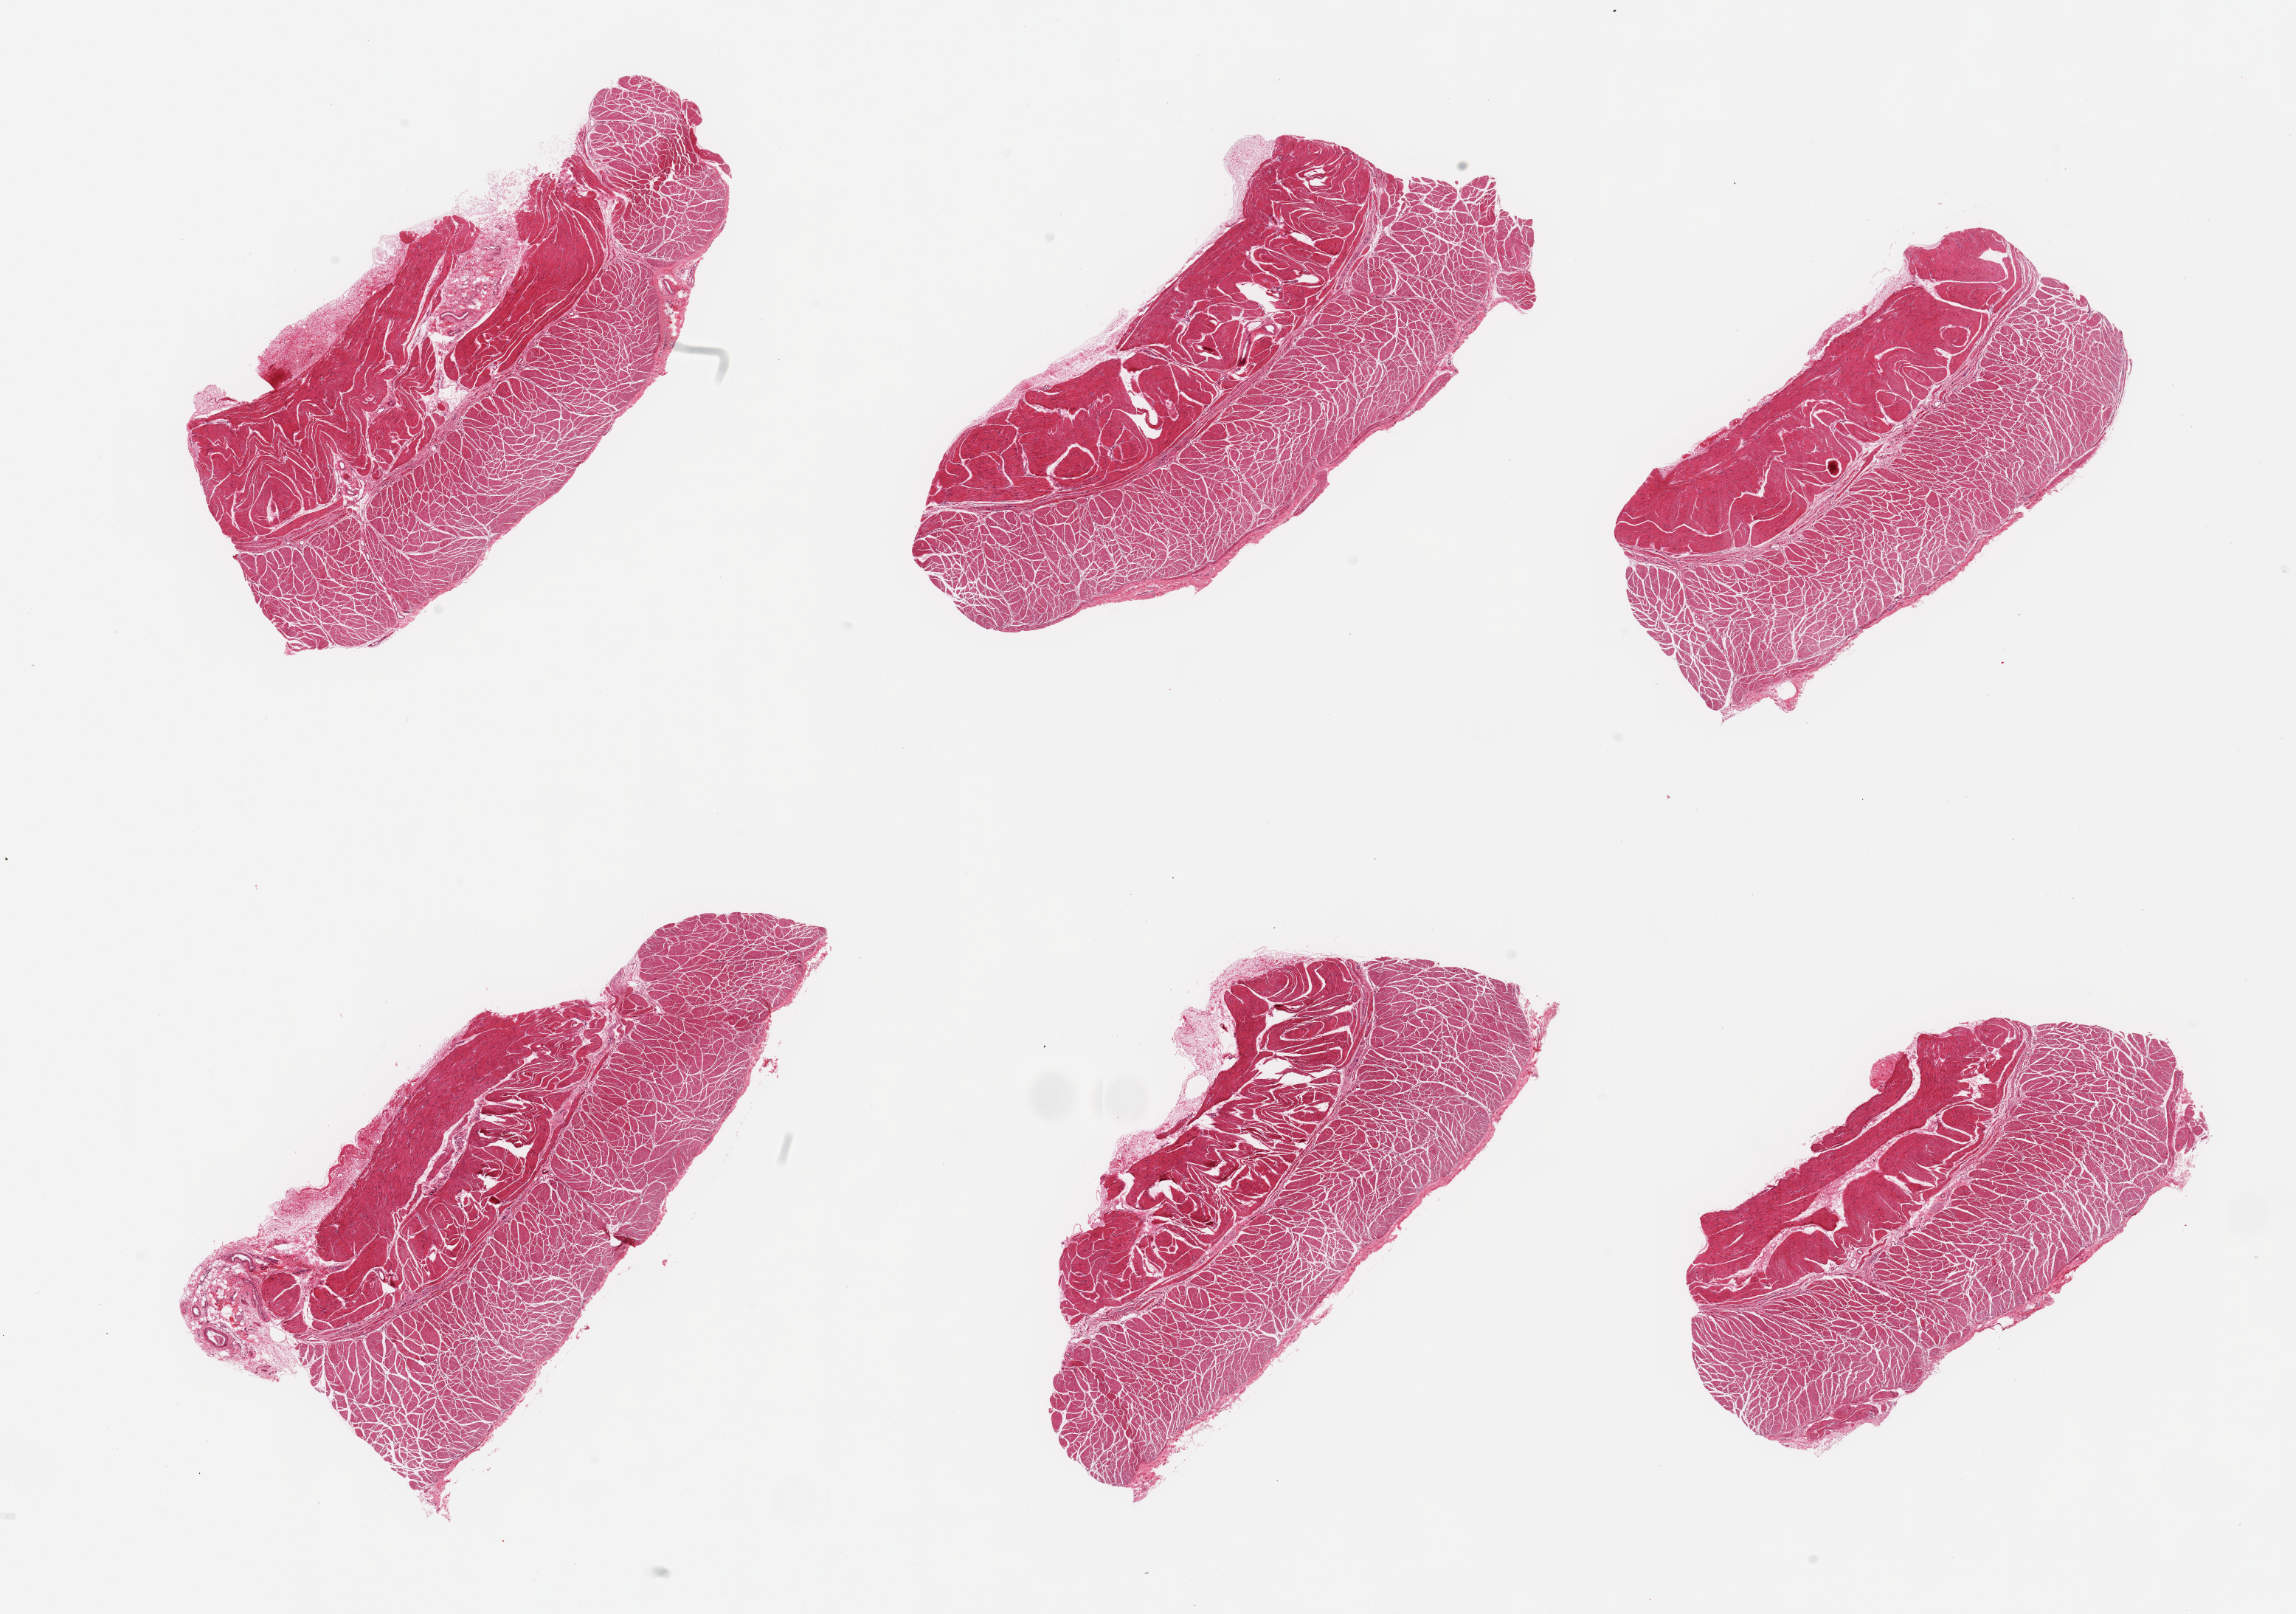
Whole-slide image, haematoxylin and eosin stain, brightfield, shown as a low-resolution overview of the whole scanned area (about 24.6 x 17.3 mm, slide scanned at 20x). PAXgene-fixed, paraffin-embedded tissue. Sampled site (target tissue): esophageal muscle. Tissue donor sample. Donor: male.
- reviewer comment on this tissue sample: 6 pieces, confirmed target muscularis